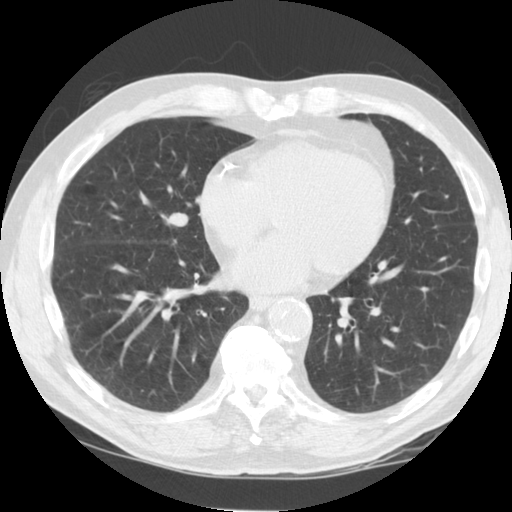
Low-dose screening chest CT, one axial slice; slice 45 of 125 in the series (ordered by position); reconstruction kernel STANDARD; 120 kVp; lung window (W 1500 / L -600 HU); 2.5 mm slice thickness; 512 × 512 image matrix.
Outlined on this slice (expert manual segmentation):
- lesion 1 (tumor, middle lobe of right lung): box from (x=161, y=213) to (x=188, y=226) px